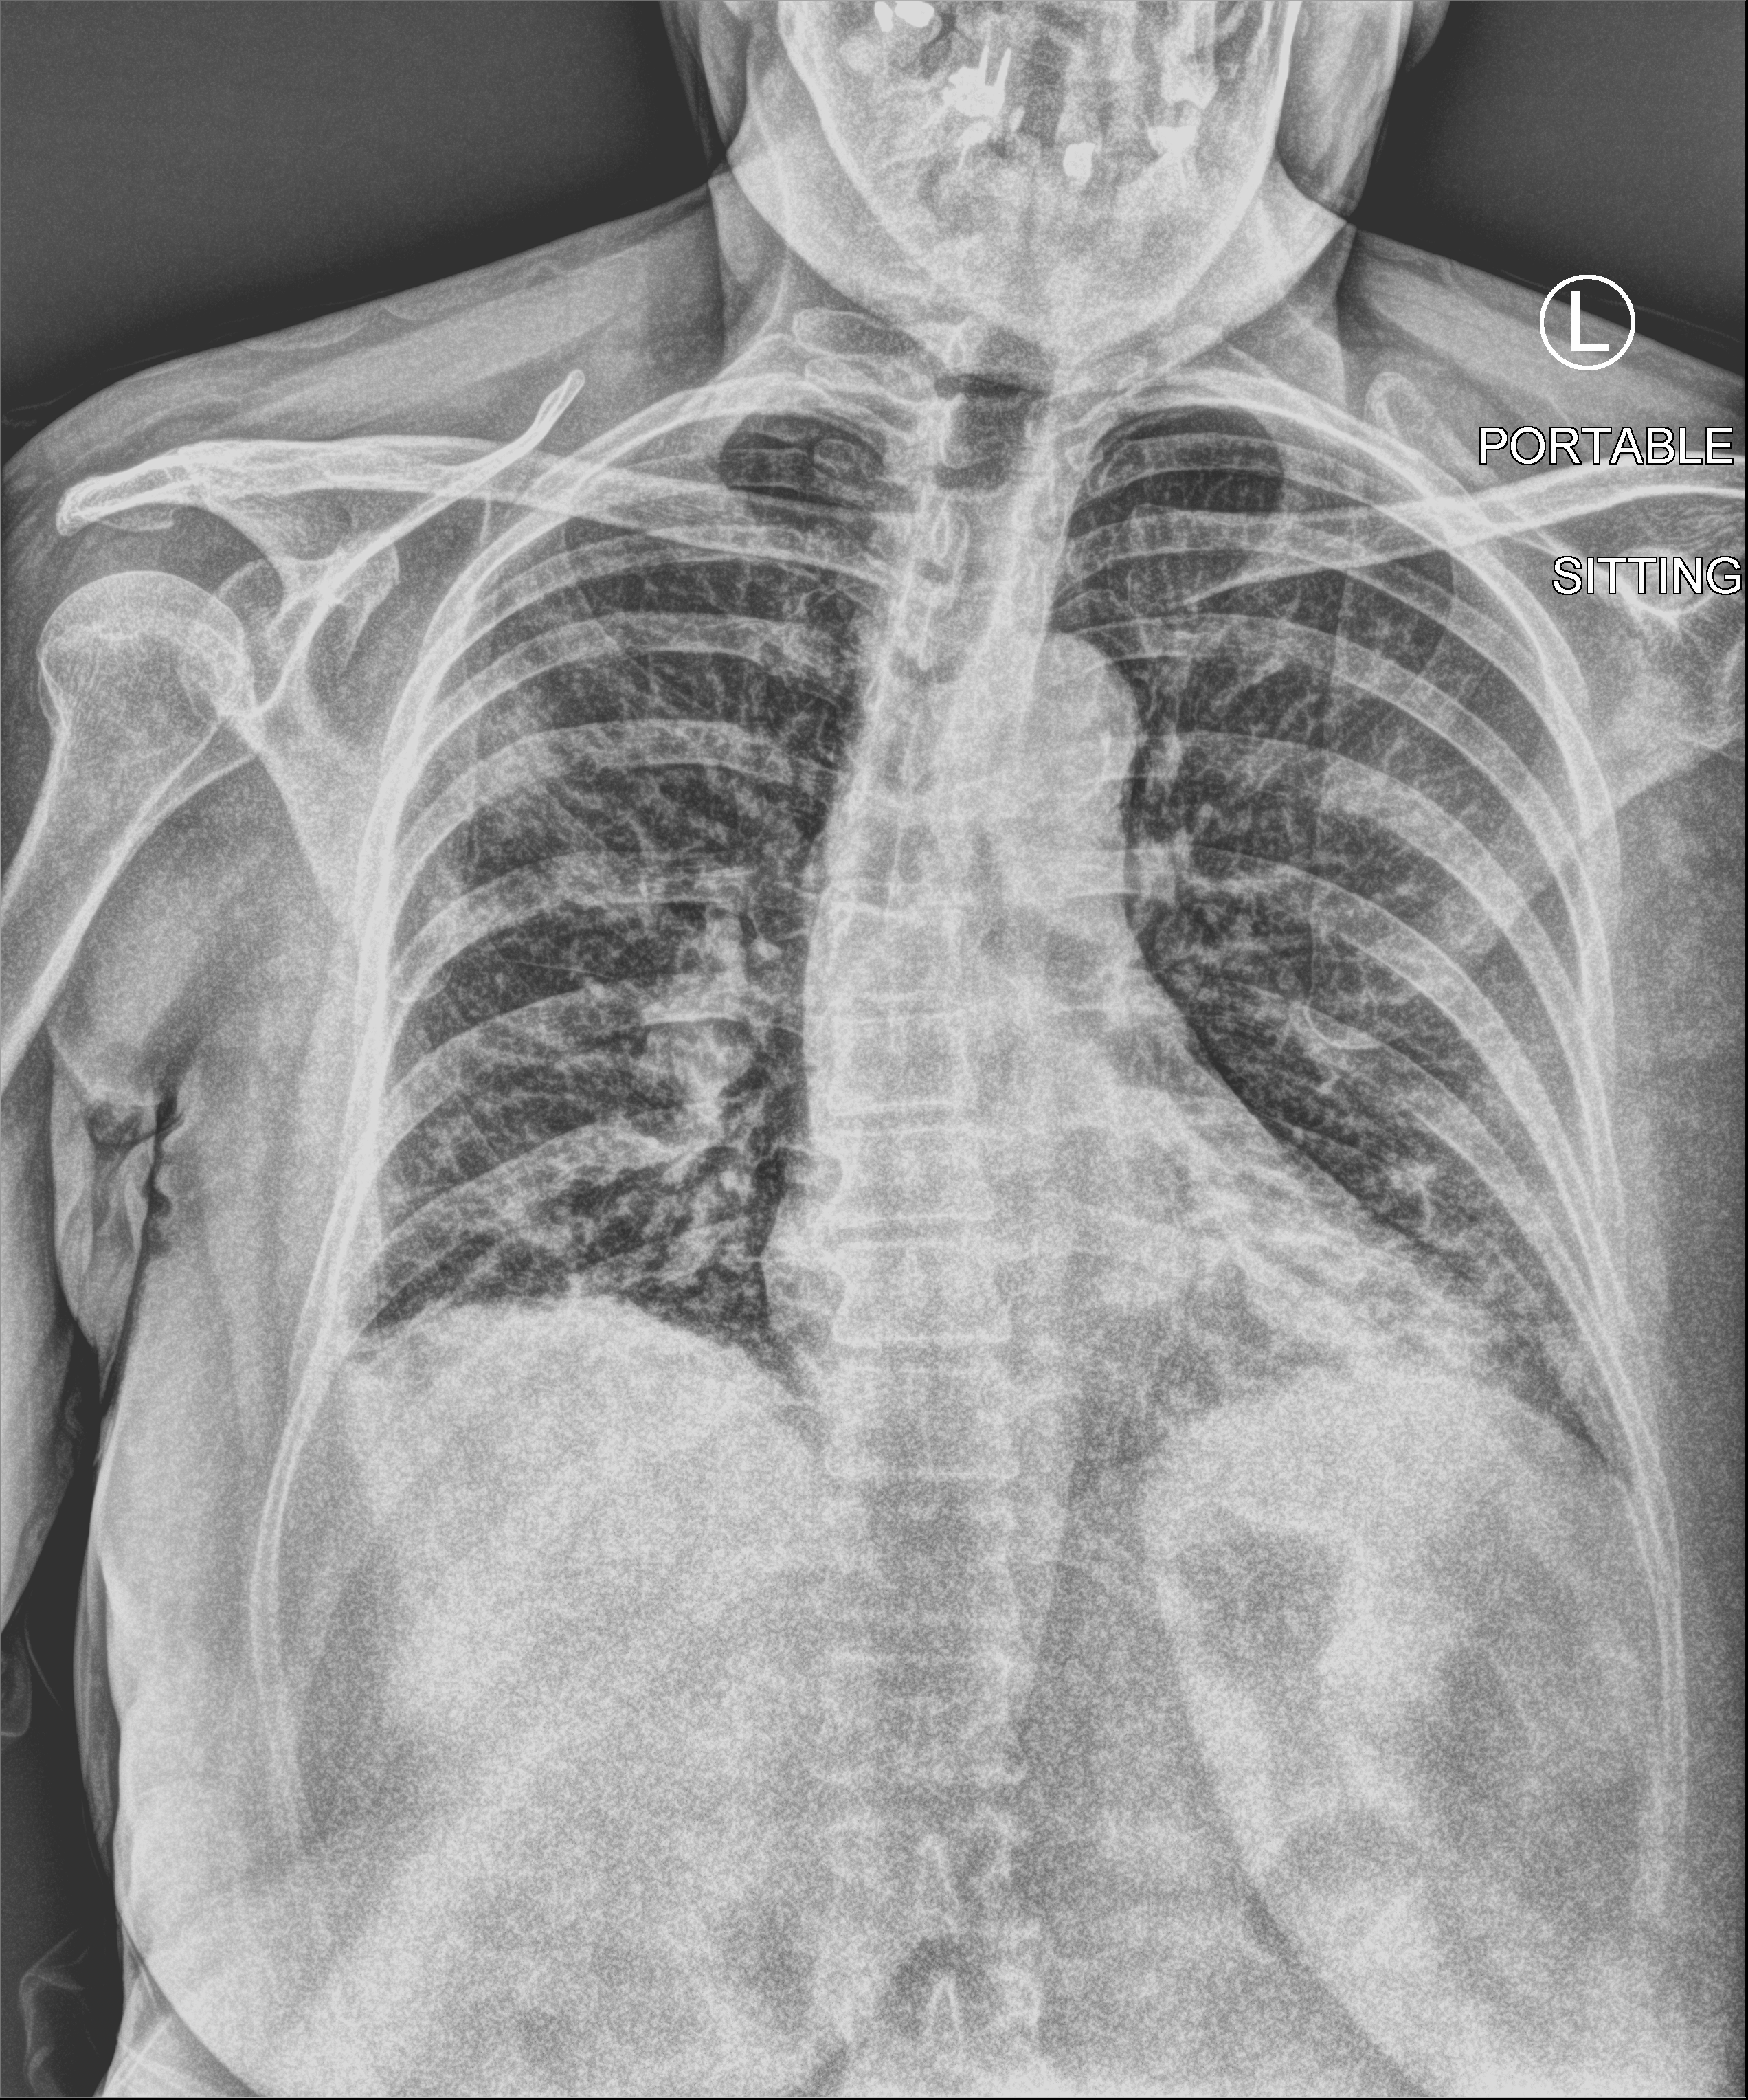
Portable chest radiograph, anteroposterior (AP) projection. Patient hospitalised with COVID-19; female, aged 60–74 years.
Admission-level facts for this patient (not findings on this image; timing relative to this image not recorded):
- admitted to intensive care during this hospital stay: no